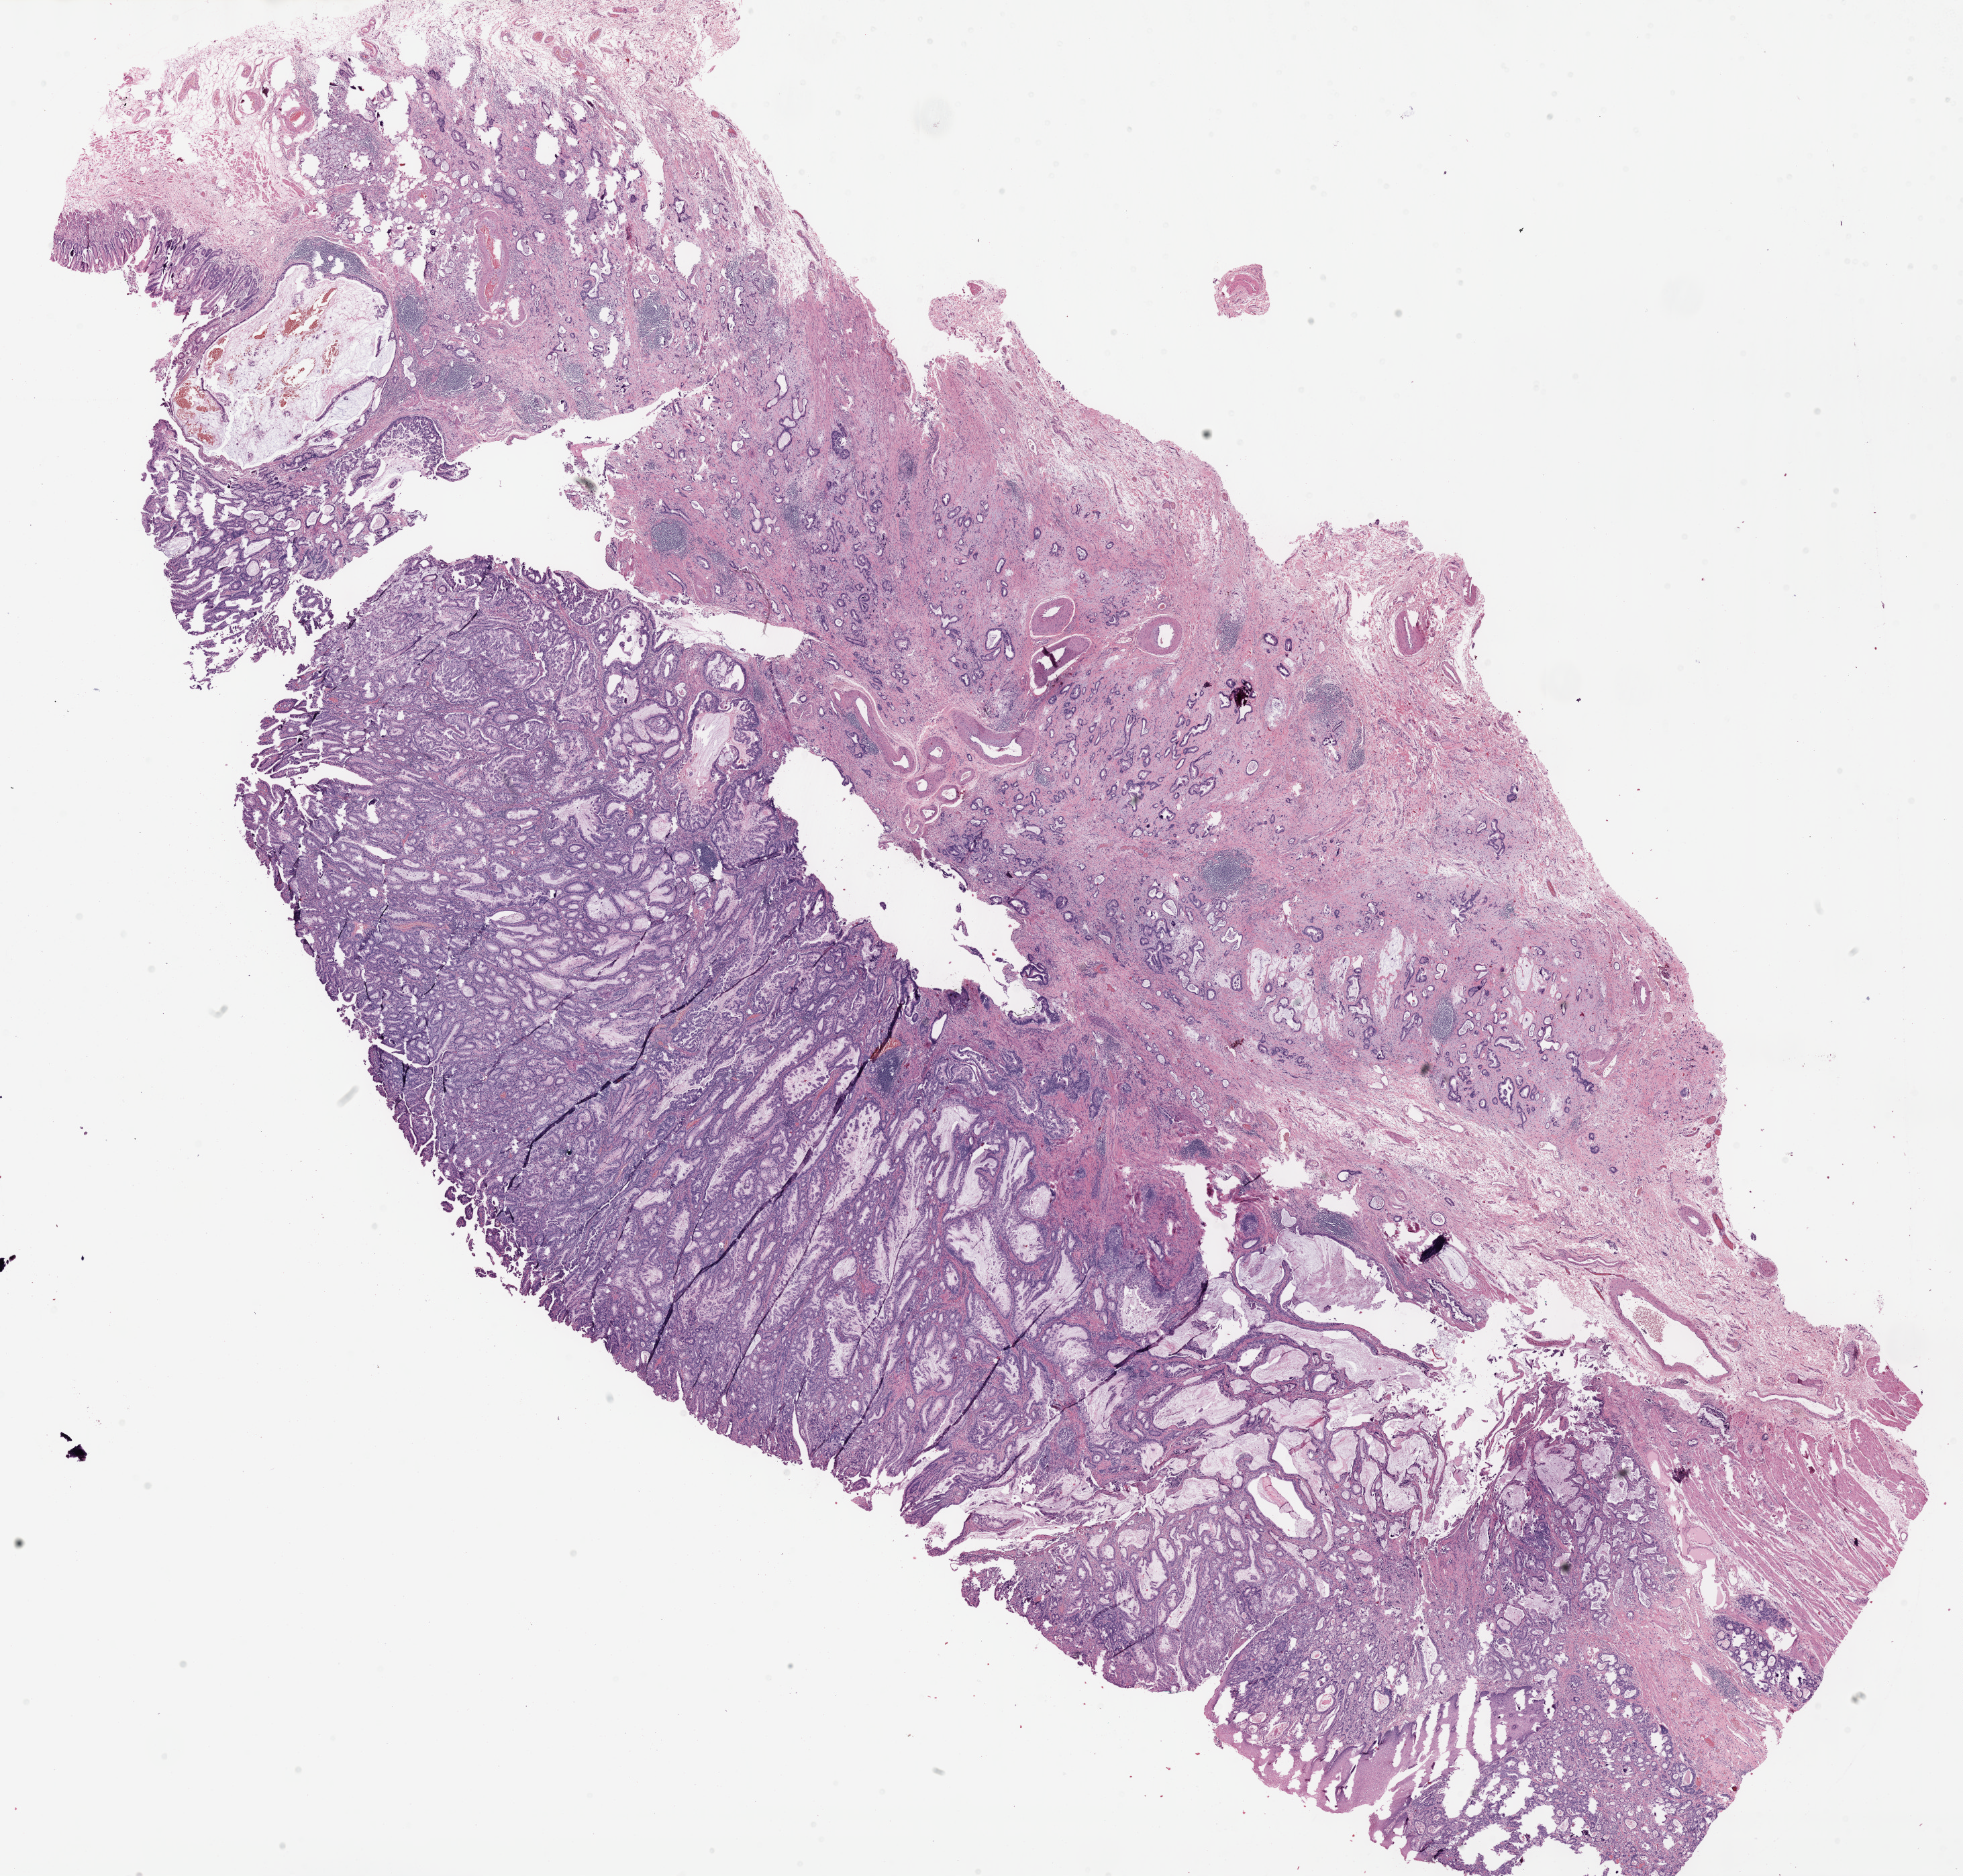
H&E-stained whole-slide image — whole scanned area (about 23.6 x 22.6 mm, acquisition: 40x scan) shown as a low-resolution overview, formalin-fixed paraffin-embedded (FFPE) diagnostic section, stomach, primary tumour sample. Patient: male, age at initial diagnosis 58 years. Histologic grade: G2 (moderately differentiated).
AJCC pathologic stage: IIIA (7th edition). Diagnosis: Tubular adenocarcinoma (cardia, NOS).